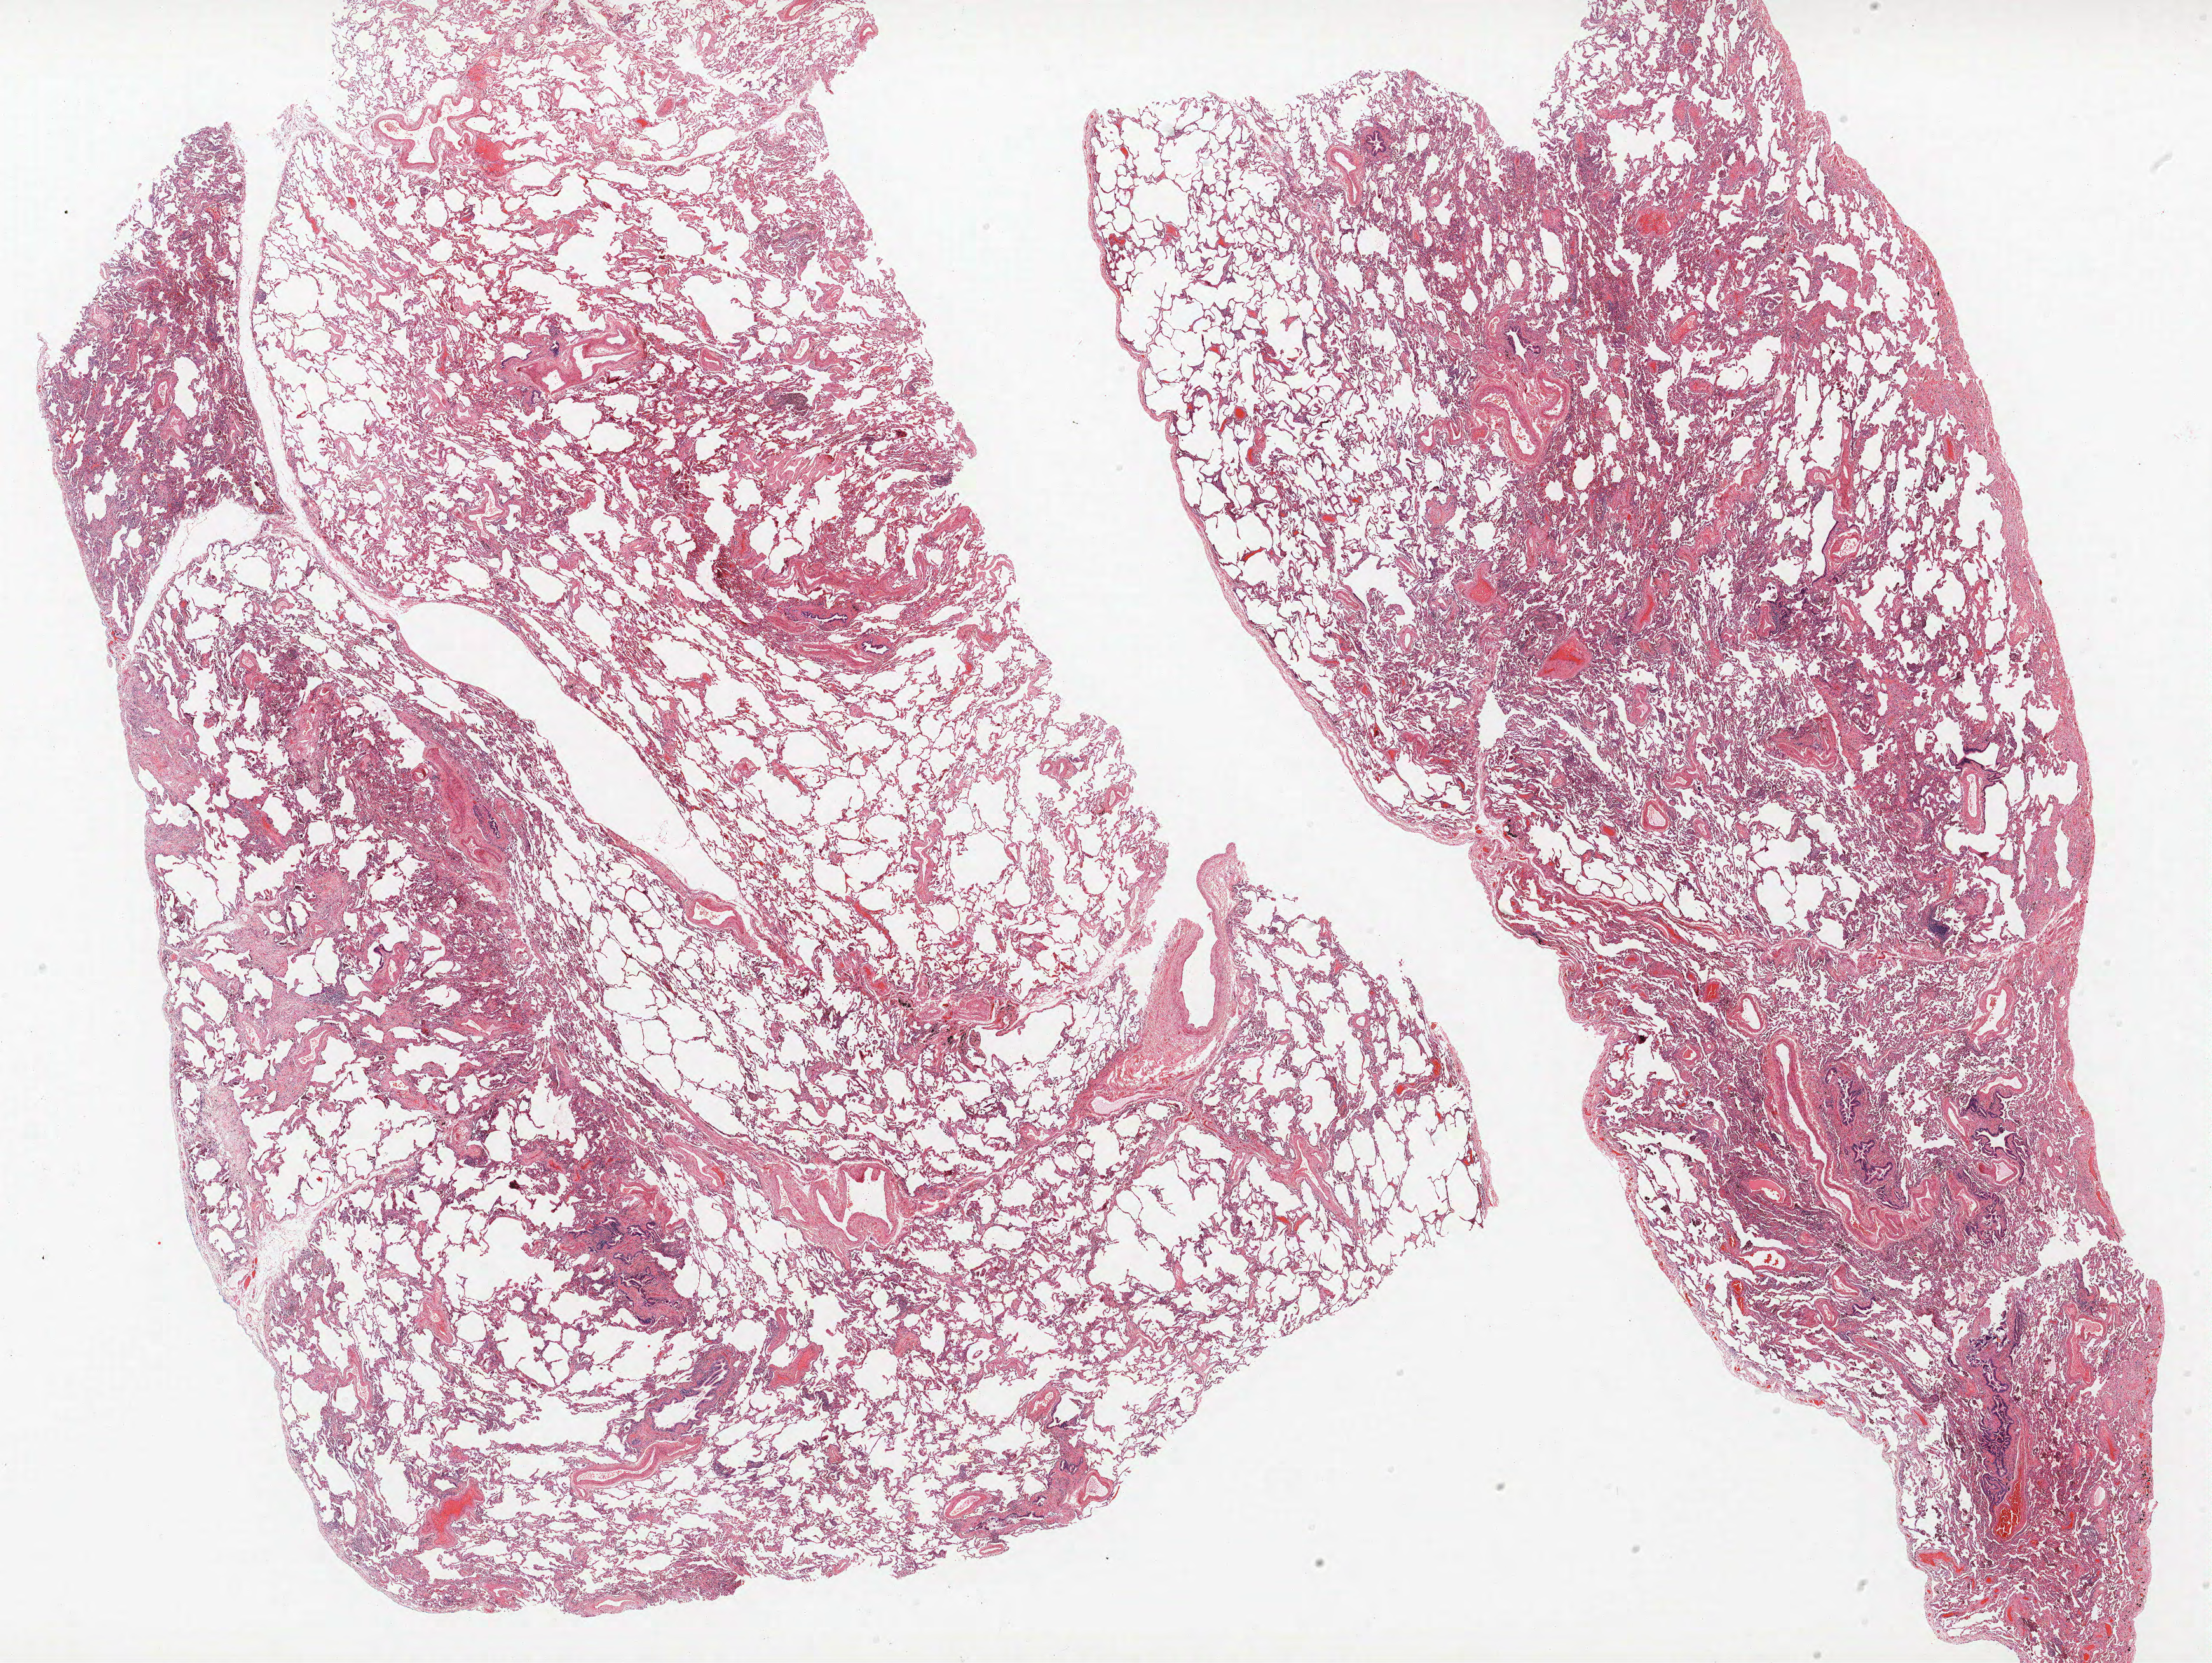
H&E-stained whole-slide image — low-resolution overview of the scanned area, about 27.8 x 20.9 mm (slide scanned at 40x); formalin-fixed paraffin-embedded (FFPE) section; lung tissue. Male, age 69 at enrolment. Grade: poorly differentiated (G3).
• tumour size (pathology): 7 mm
• stage (AJCC 6th edition): IA
• ICD-O-3 topography: upper lobe of lung (C34.1)
• participant's lung-cancer diagnosis: Squamous cell carcinoma, large cell, nonkeratinizing, NOS (ICD-O-3 8072/3)
• primary tumour location (clinical record): right upper lobe